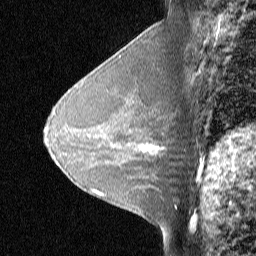
Breast MRI (dynamic contrast-enhanced), one sagittal slice; slice 29 of 48 in the series (ordered by position); dynamic contrast-enhanced study with each time point stored as its own series, time point 2 of 3 at this slice position (early post-contrast, ordered by acquisition time); 1.5 T; TE 4 ms, TR 30 ms; 3 mm slice thickness; 256 × 256 image matrix, field of view 180 × 180 mm. Female patient, age 31 years. From the clinical record (not read from this slice): setting: breast cancer imaged before/during neoadjuvant chemotherapy; receptor status: HER2-positive.
Structures marked on this image (semi-automatic segmentation, software-assisted and operator-edited):
- analysis volume of interest (the breast-tissue region the enhancement analysis was run in; not a lesion): bounding box [x1, y1, x2, y2] px = [129, 130, 175, 167]
- tumour enhancement mask (voxels above the 90 % enhancement threshold inside the analysis volume of interest): [142, 145, 162, 154]